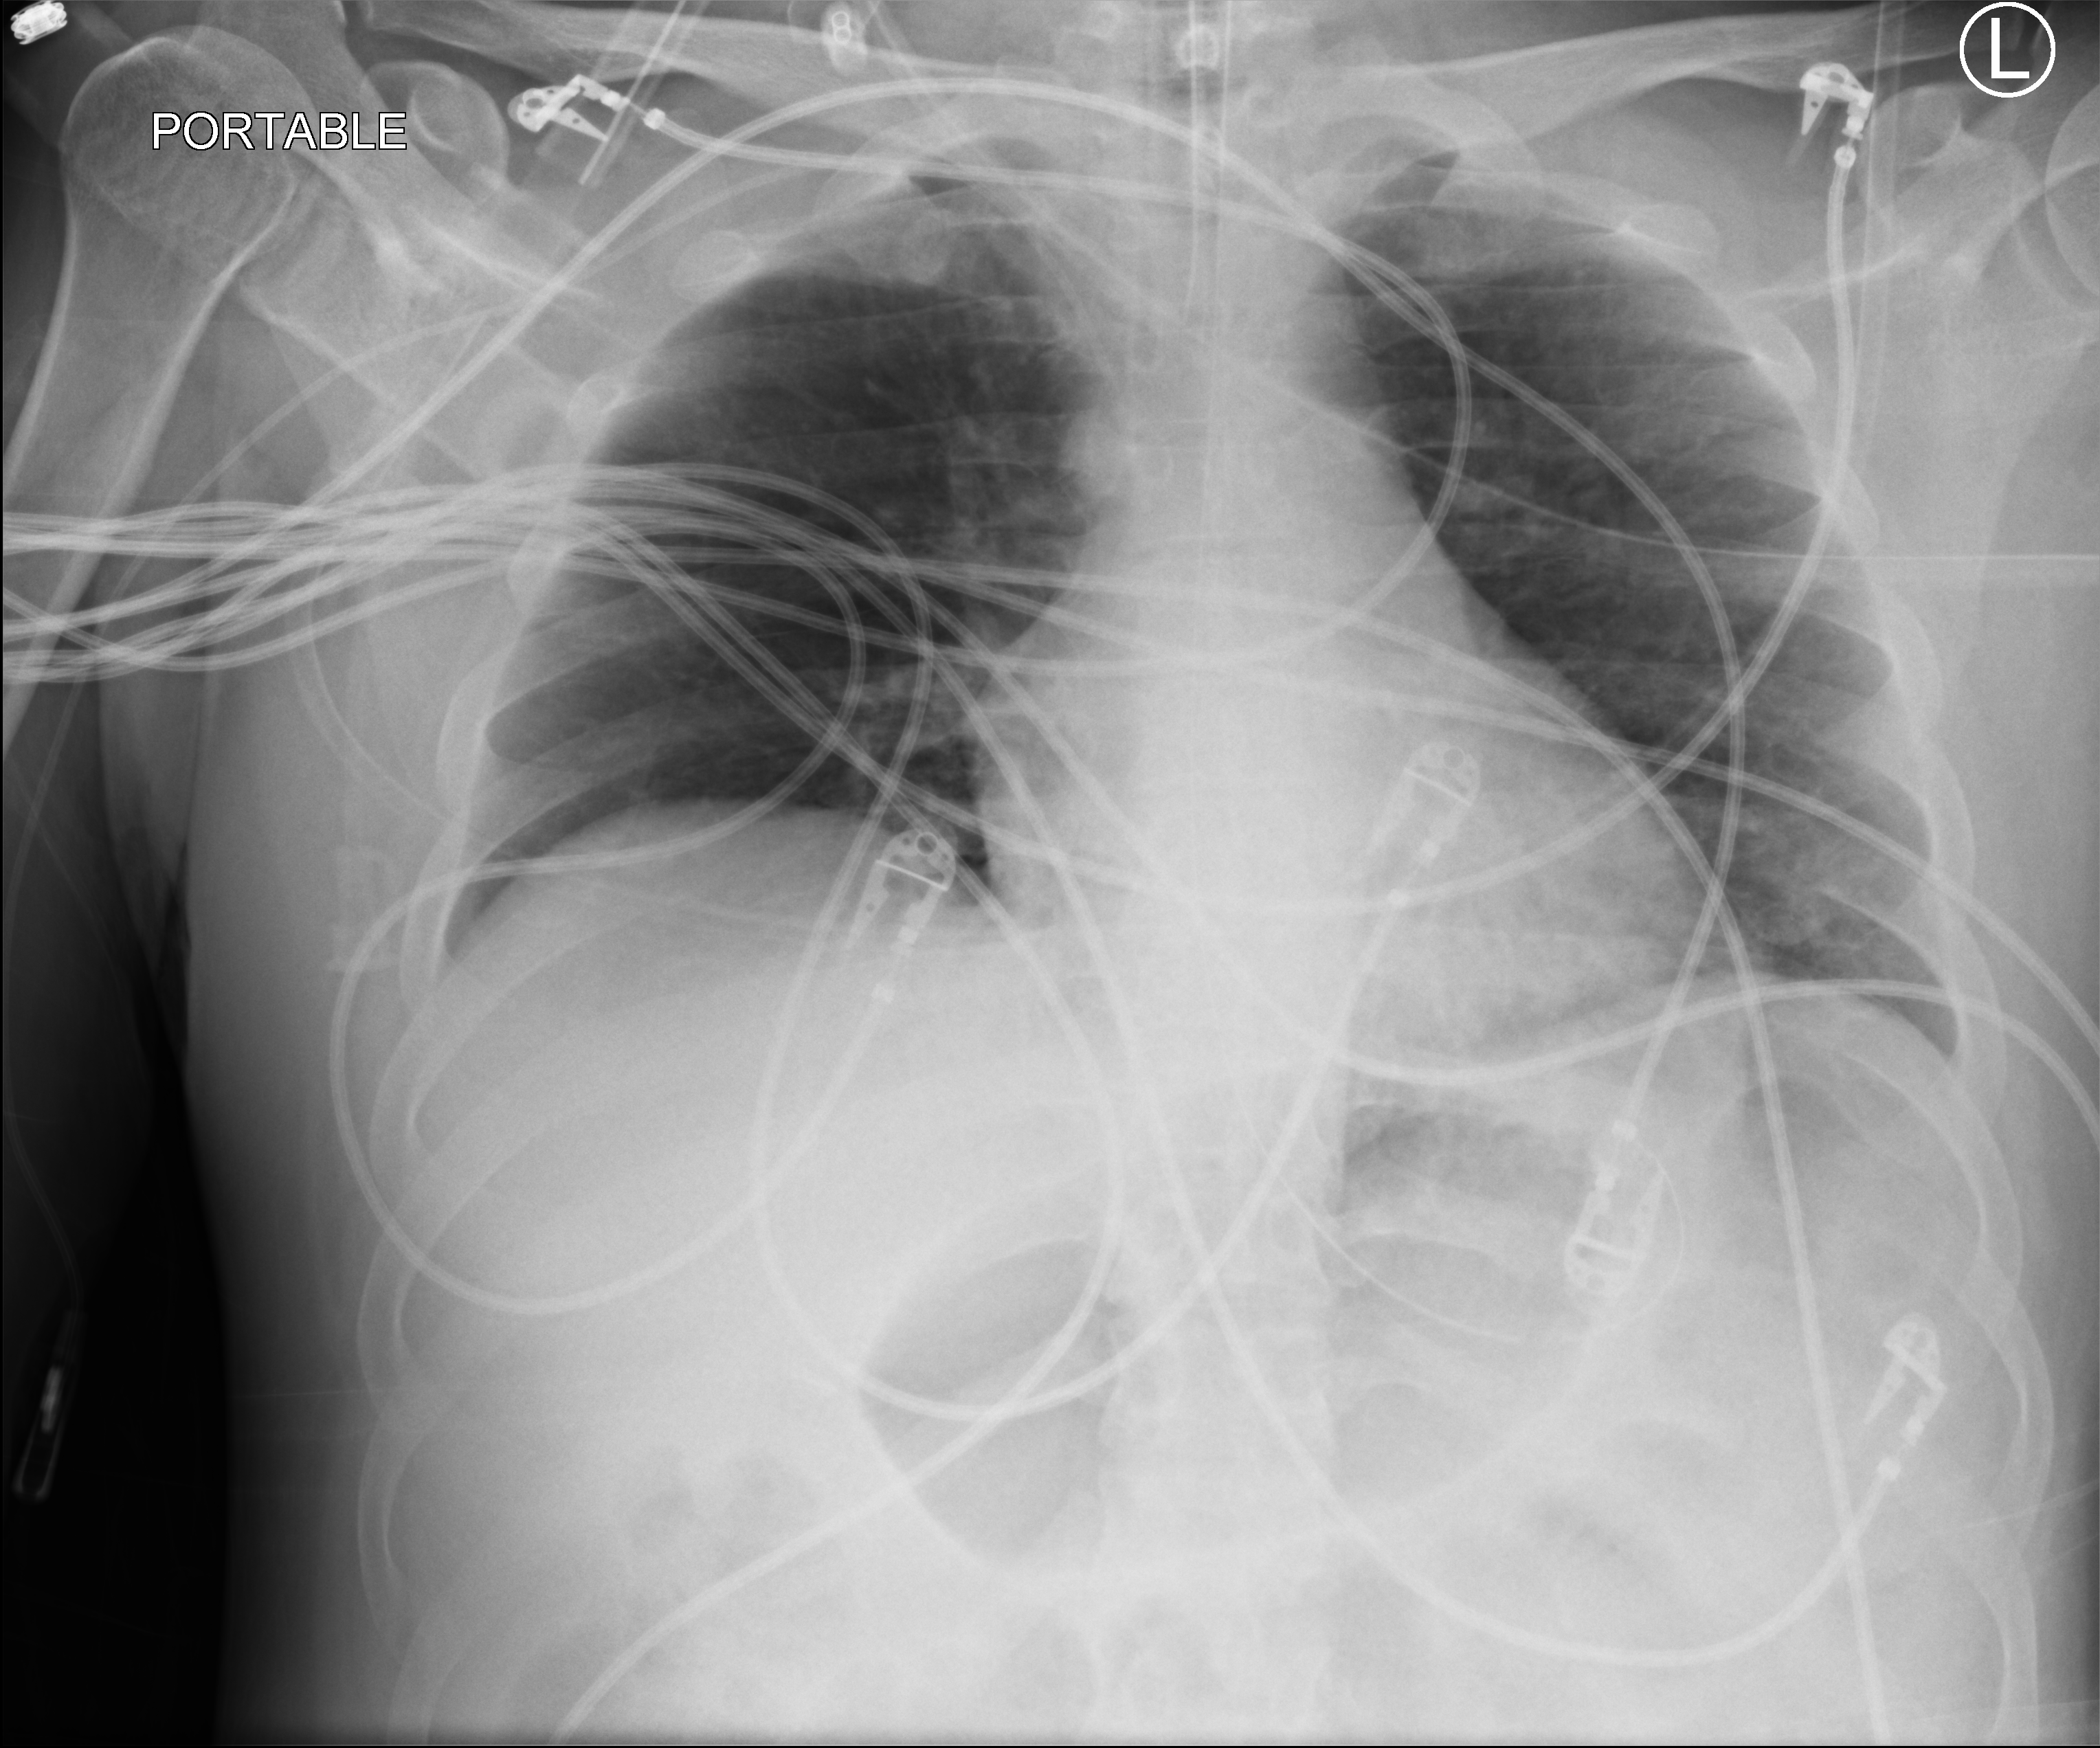
Bedside chest radiograph (computed radiography); anteroposterior (AP) projection. Male patient hospitalised with COVID-19, age 18–59 years.
Hospital-stay facts (about this admission, not read from this image; timing relative to this image not recorded):
- mechanically ventilated during this hospital stay: yes